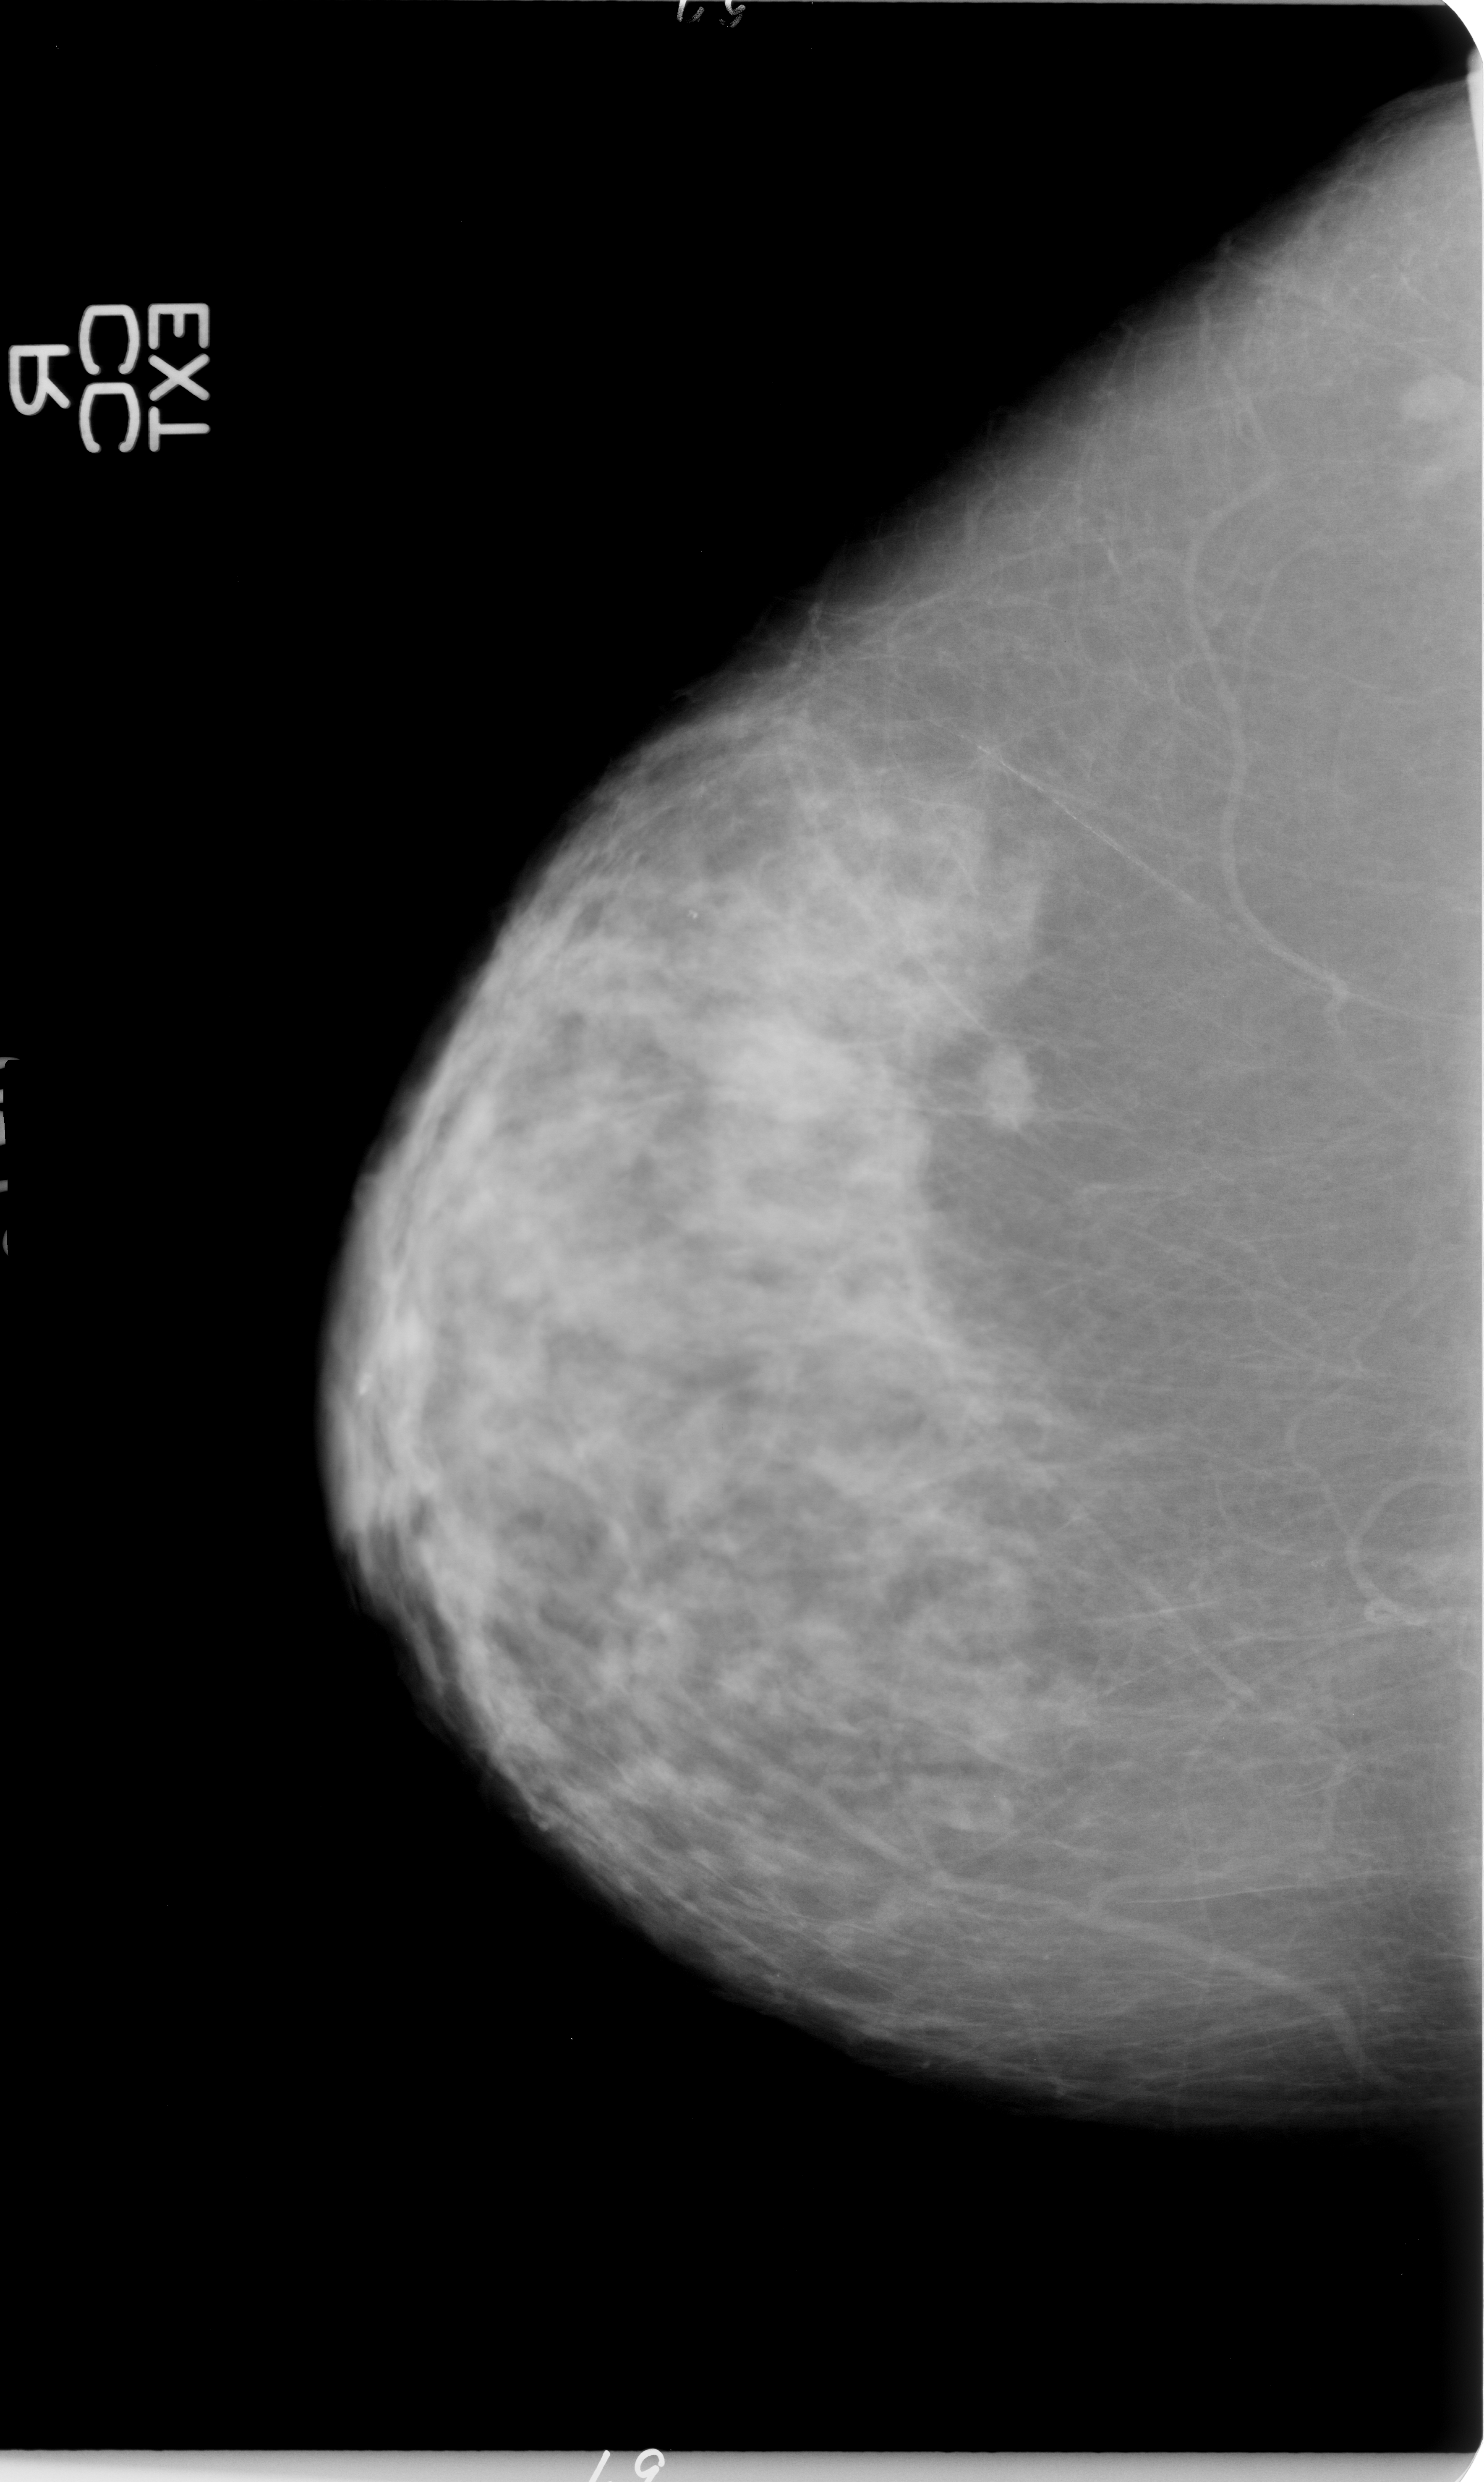
Digitized screen-film mammogram, right breast, craniocaudal (CC) view, BI-RADS breast density category 3 (scale 1–4).
Finding: mass, shape irregular, margins microlobulated; BI-RADS assessment category 4; pathology result (as recorded, not read from the image): malignant.